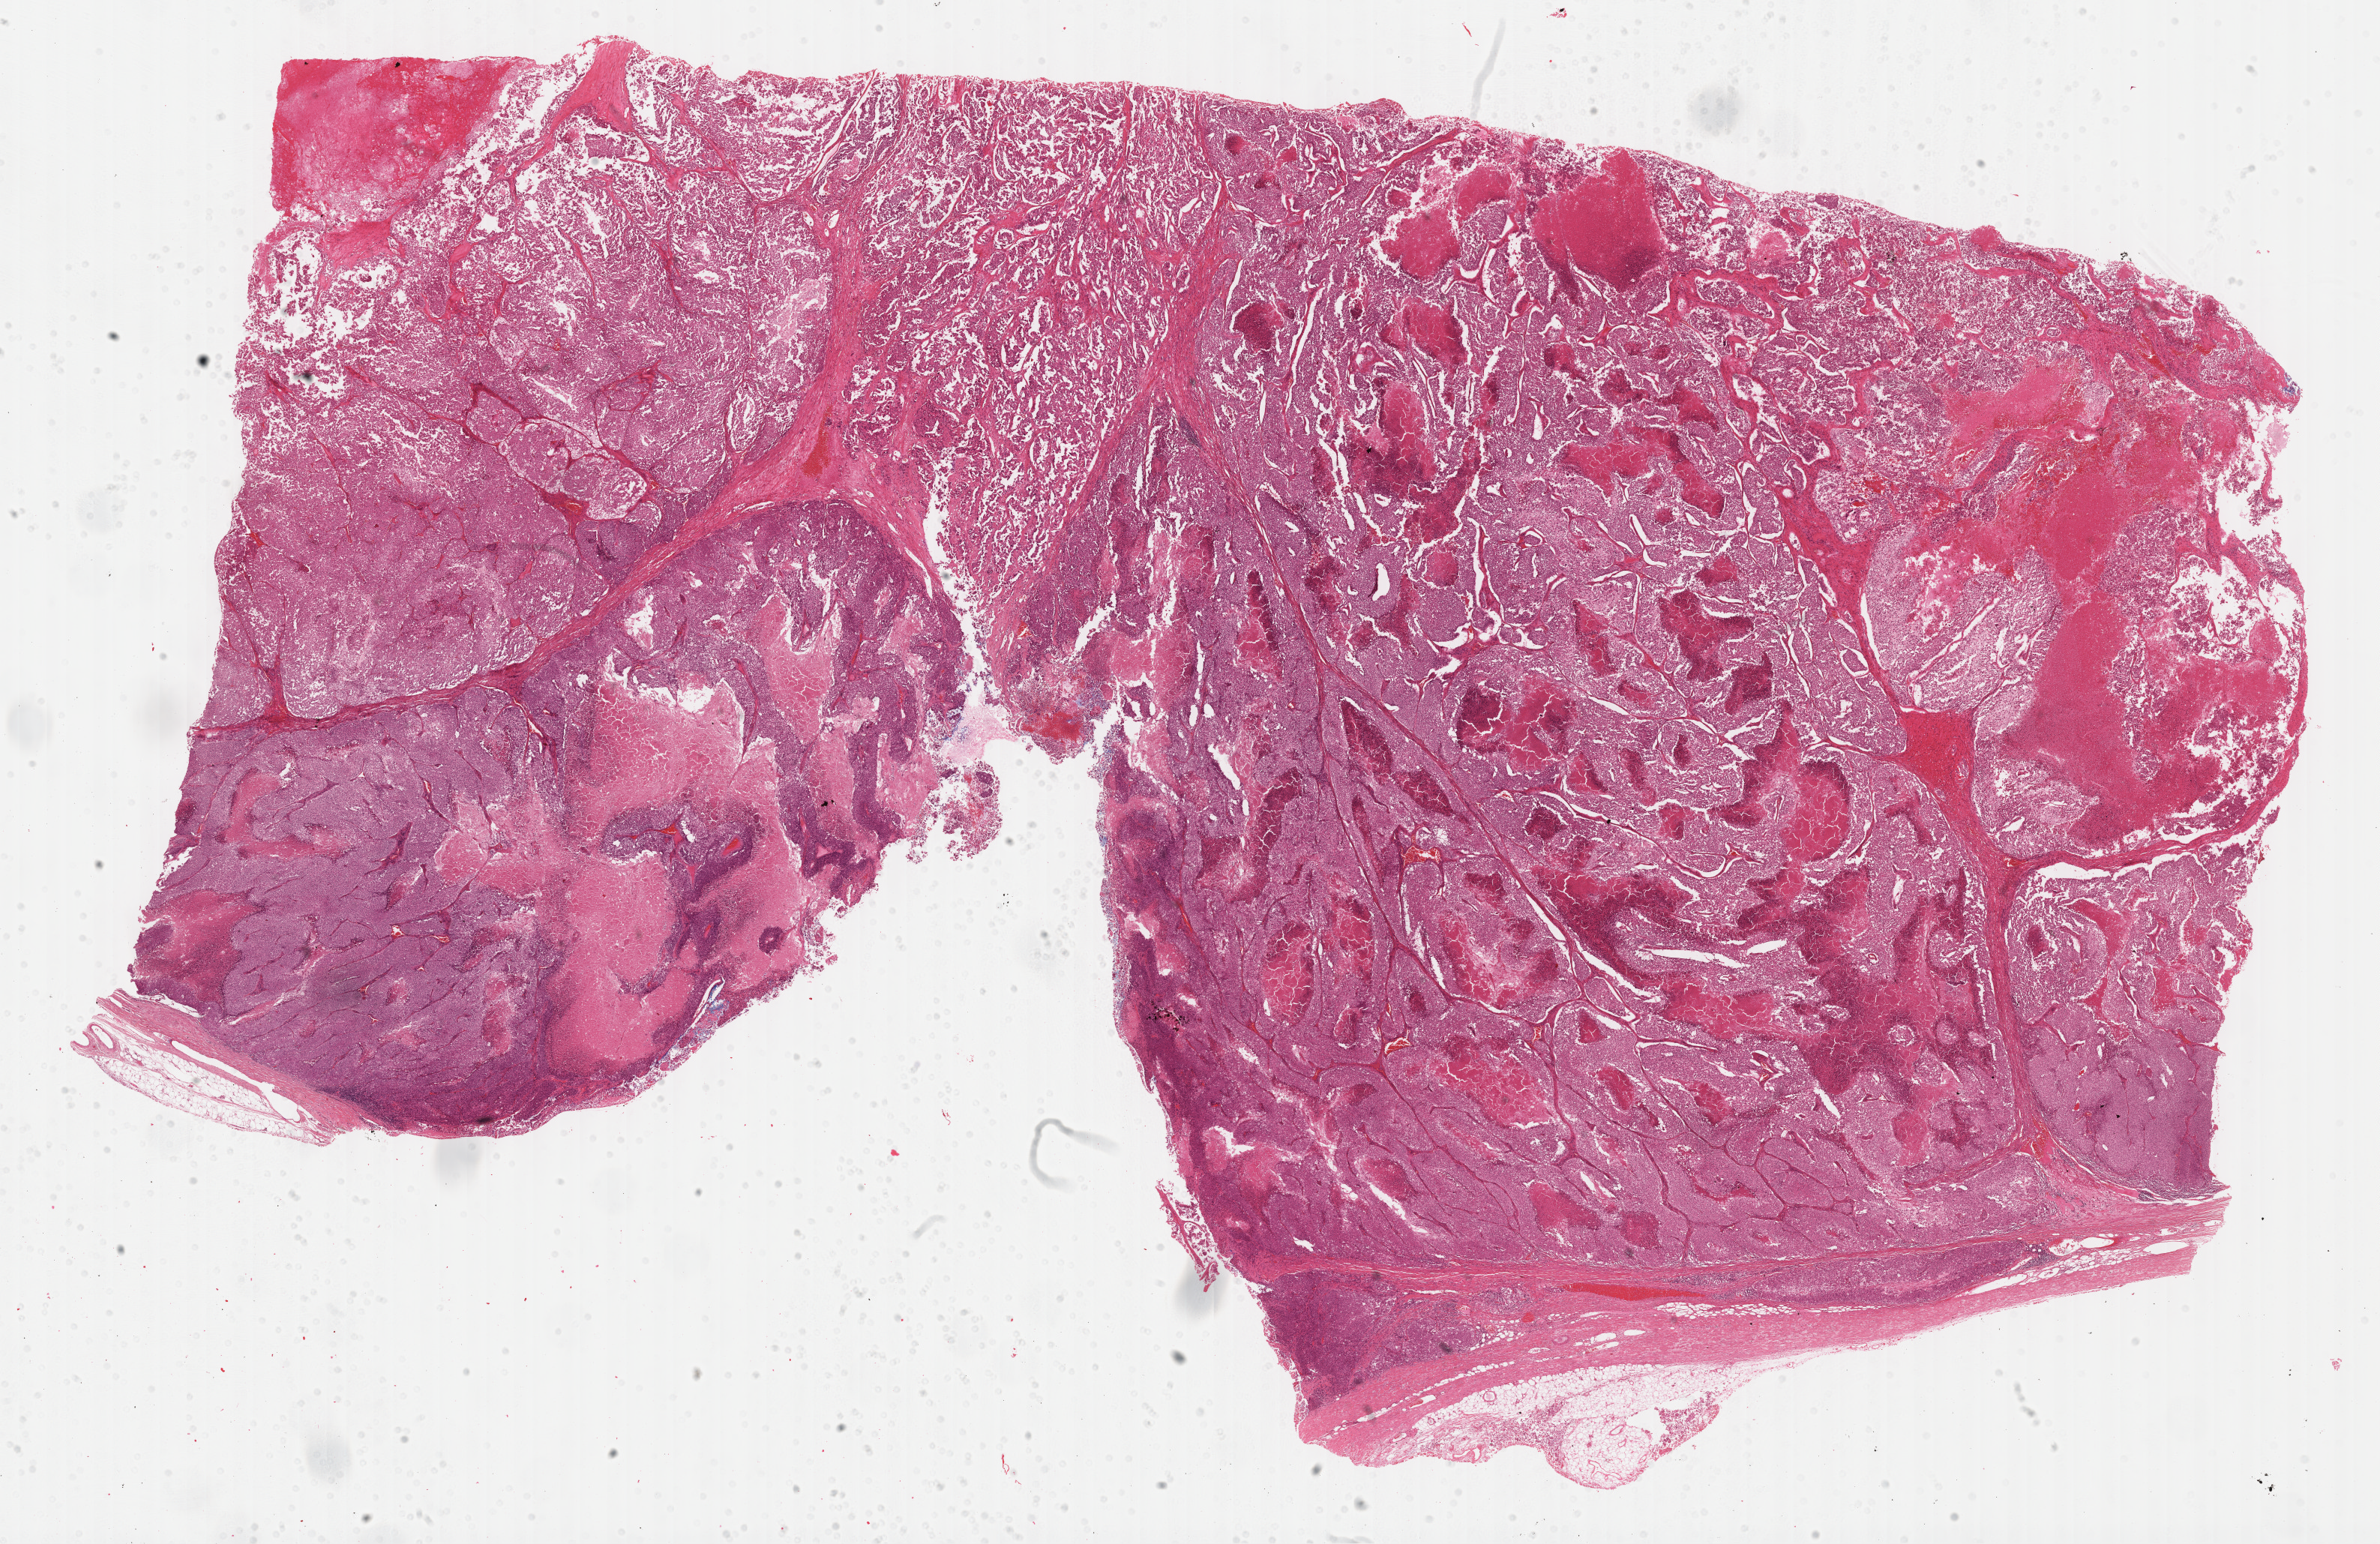
Digitized H&E tissue section (whole slide) — shown as a low-resolution overview of the whole scanned area (about 25.7 x 16.7 mm); formalin-fixed paraffin-embedded (FFPE) diagnostic section; adrenal cortex, primary tumour sample. Patient: male, age at initial diagnosis 65 years.
* lymph nodes positive (case pathology): 6 of 6 examined
* diagnosis: Adrenal cortical carcinoma (cortex of adrenal gland)